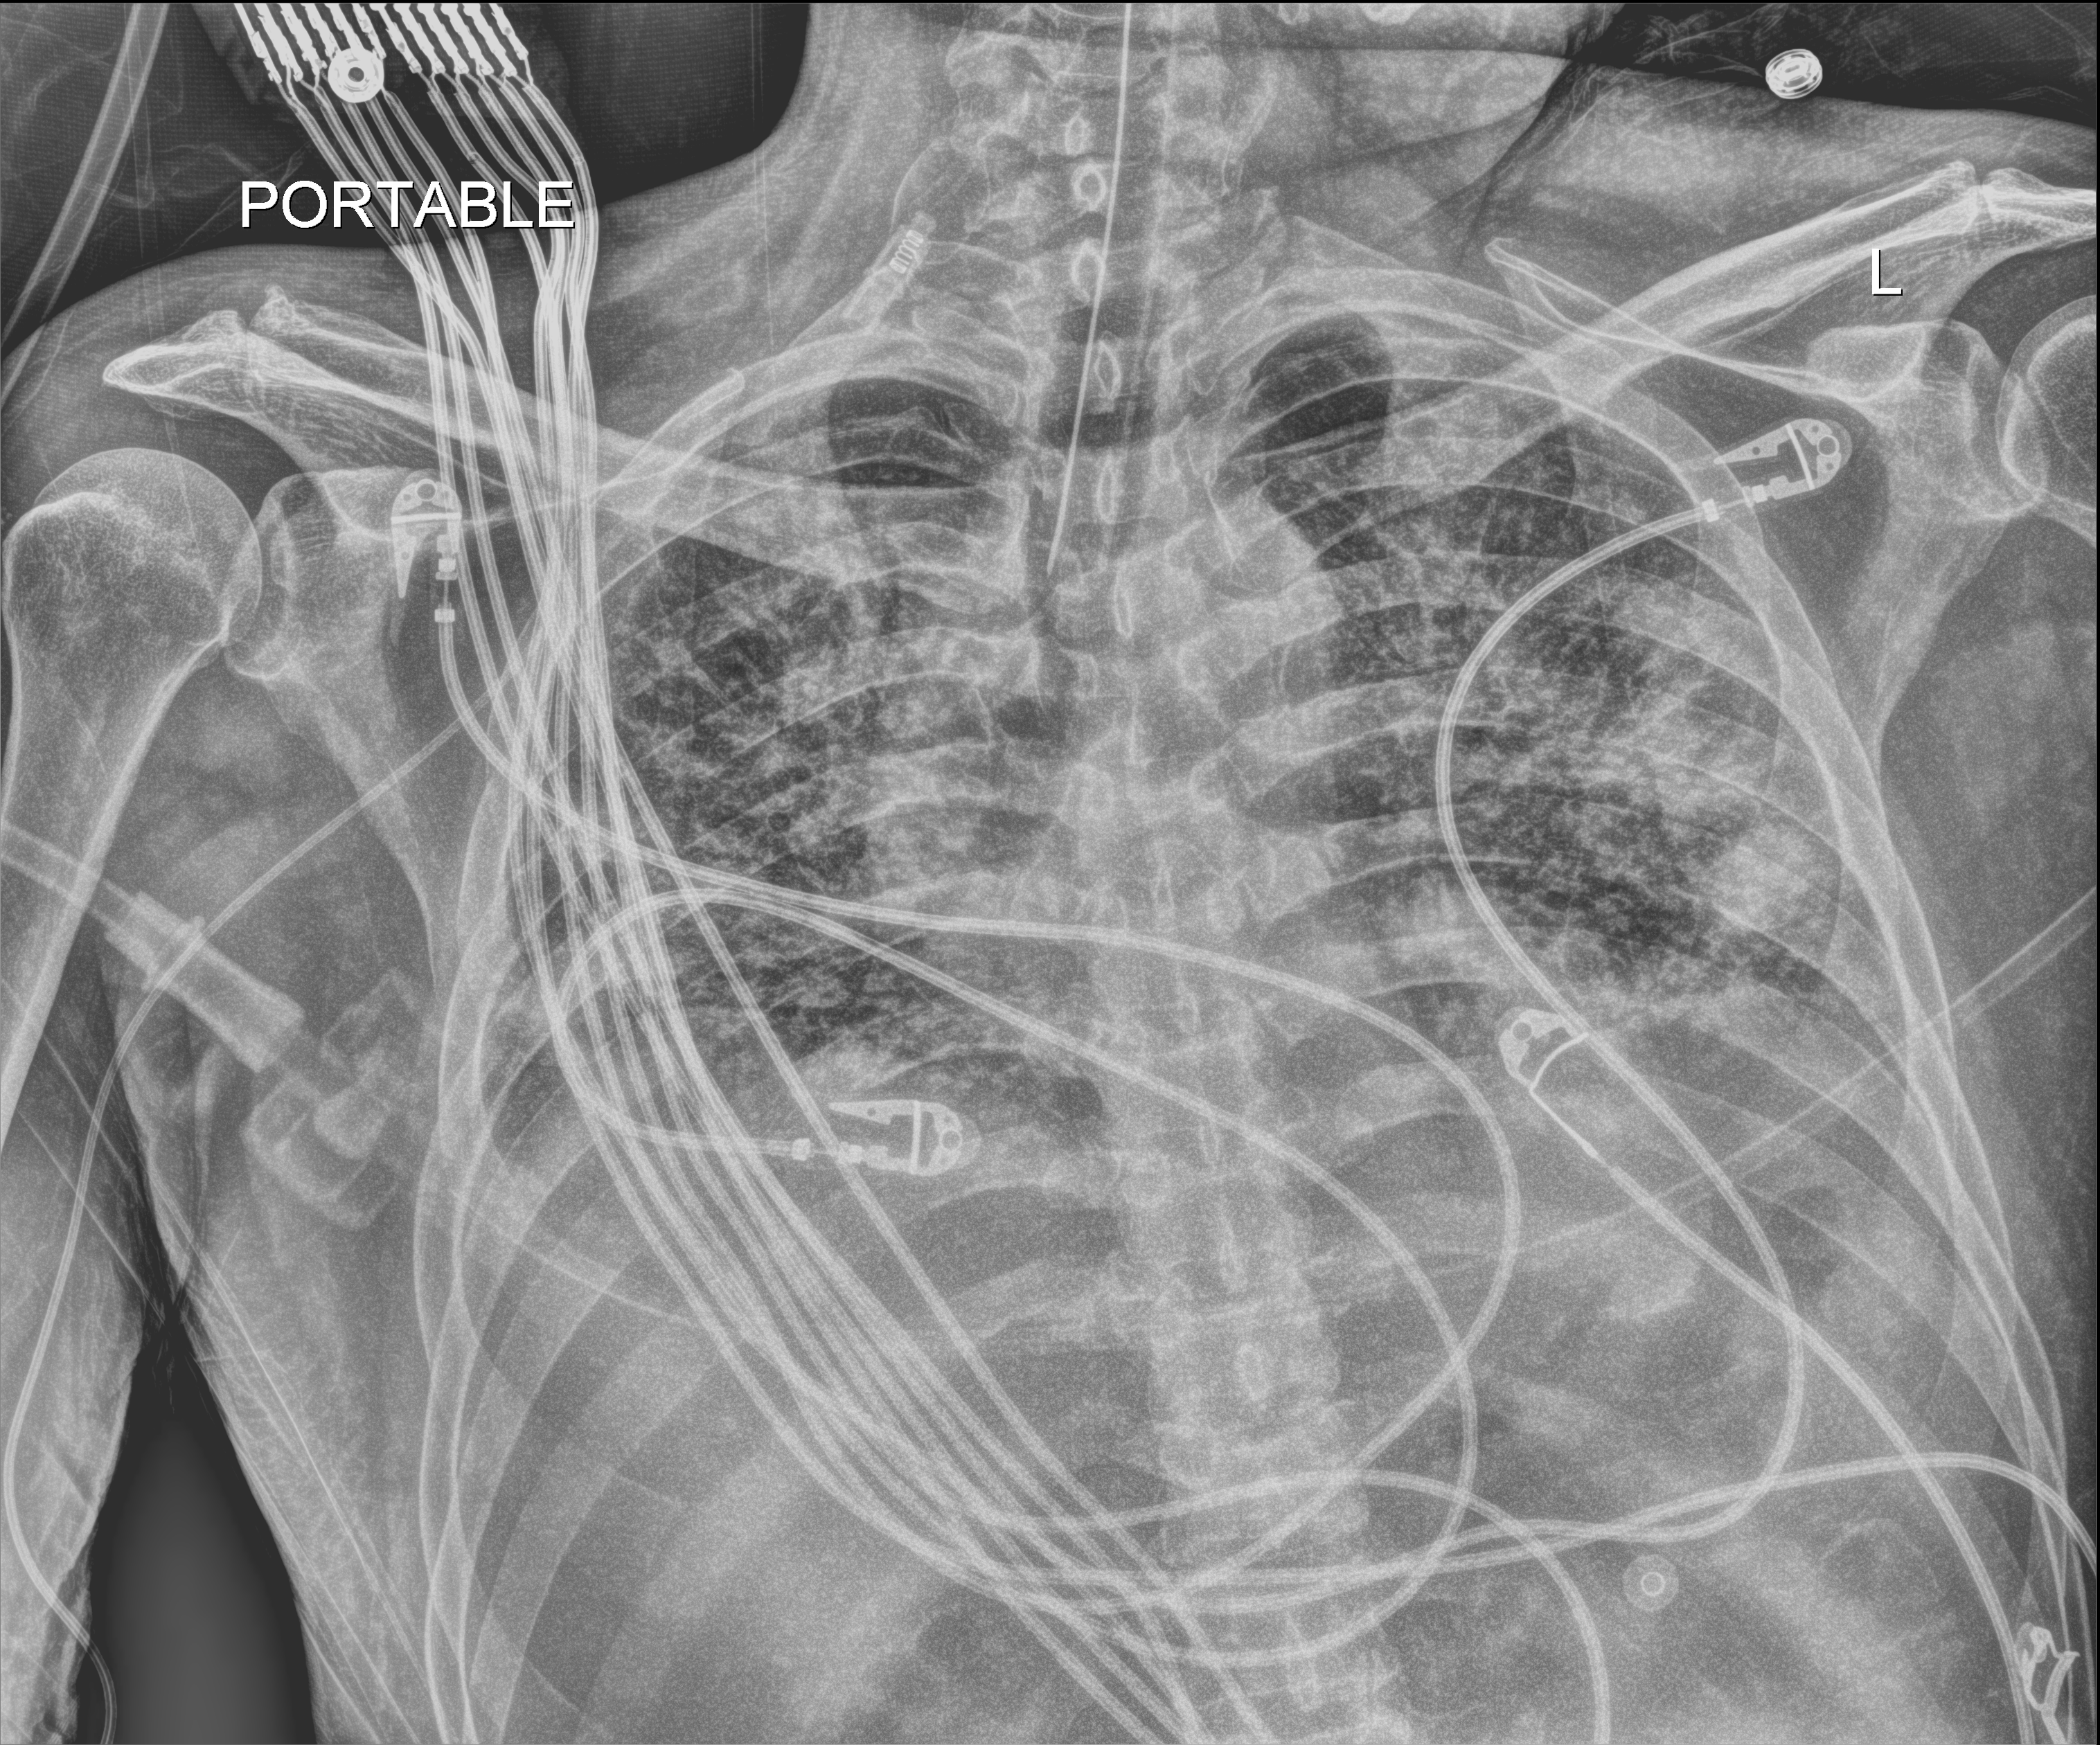
Chest X-ray (portable), anteroposterior (AP) projection. Male patient hospitalised with COVID-19, age 18–59 years.
Hospital-stay facts (about this admission, not read from this image; timing relative to this image not recorded): mechanically ventilated during this hospital stay: yes; admitted to intensive care during this hospital stay: yes.